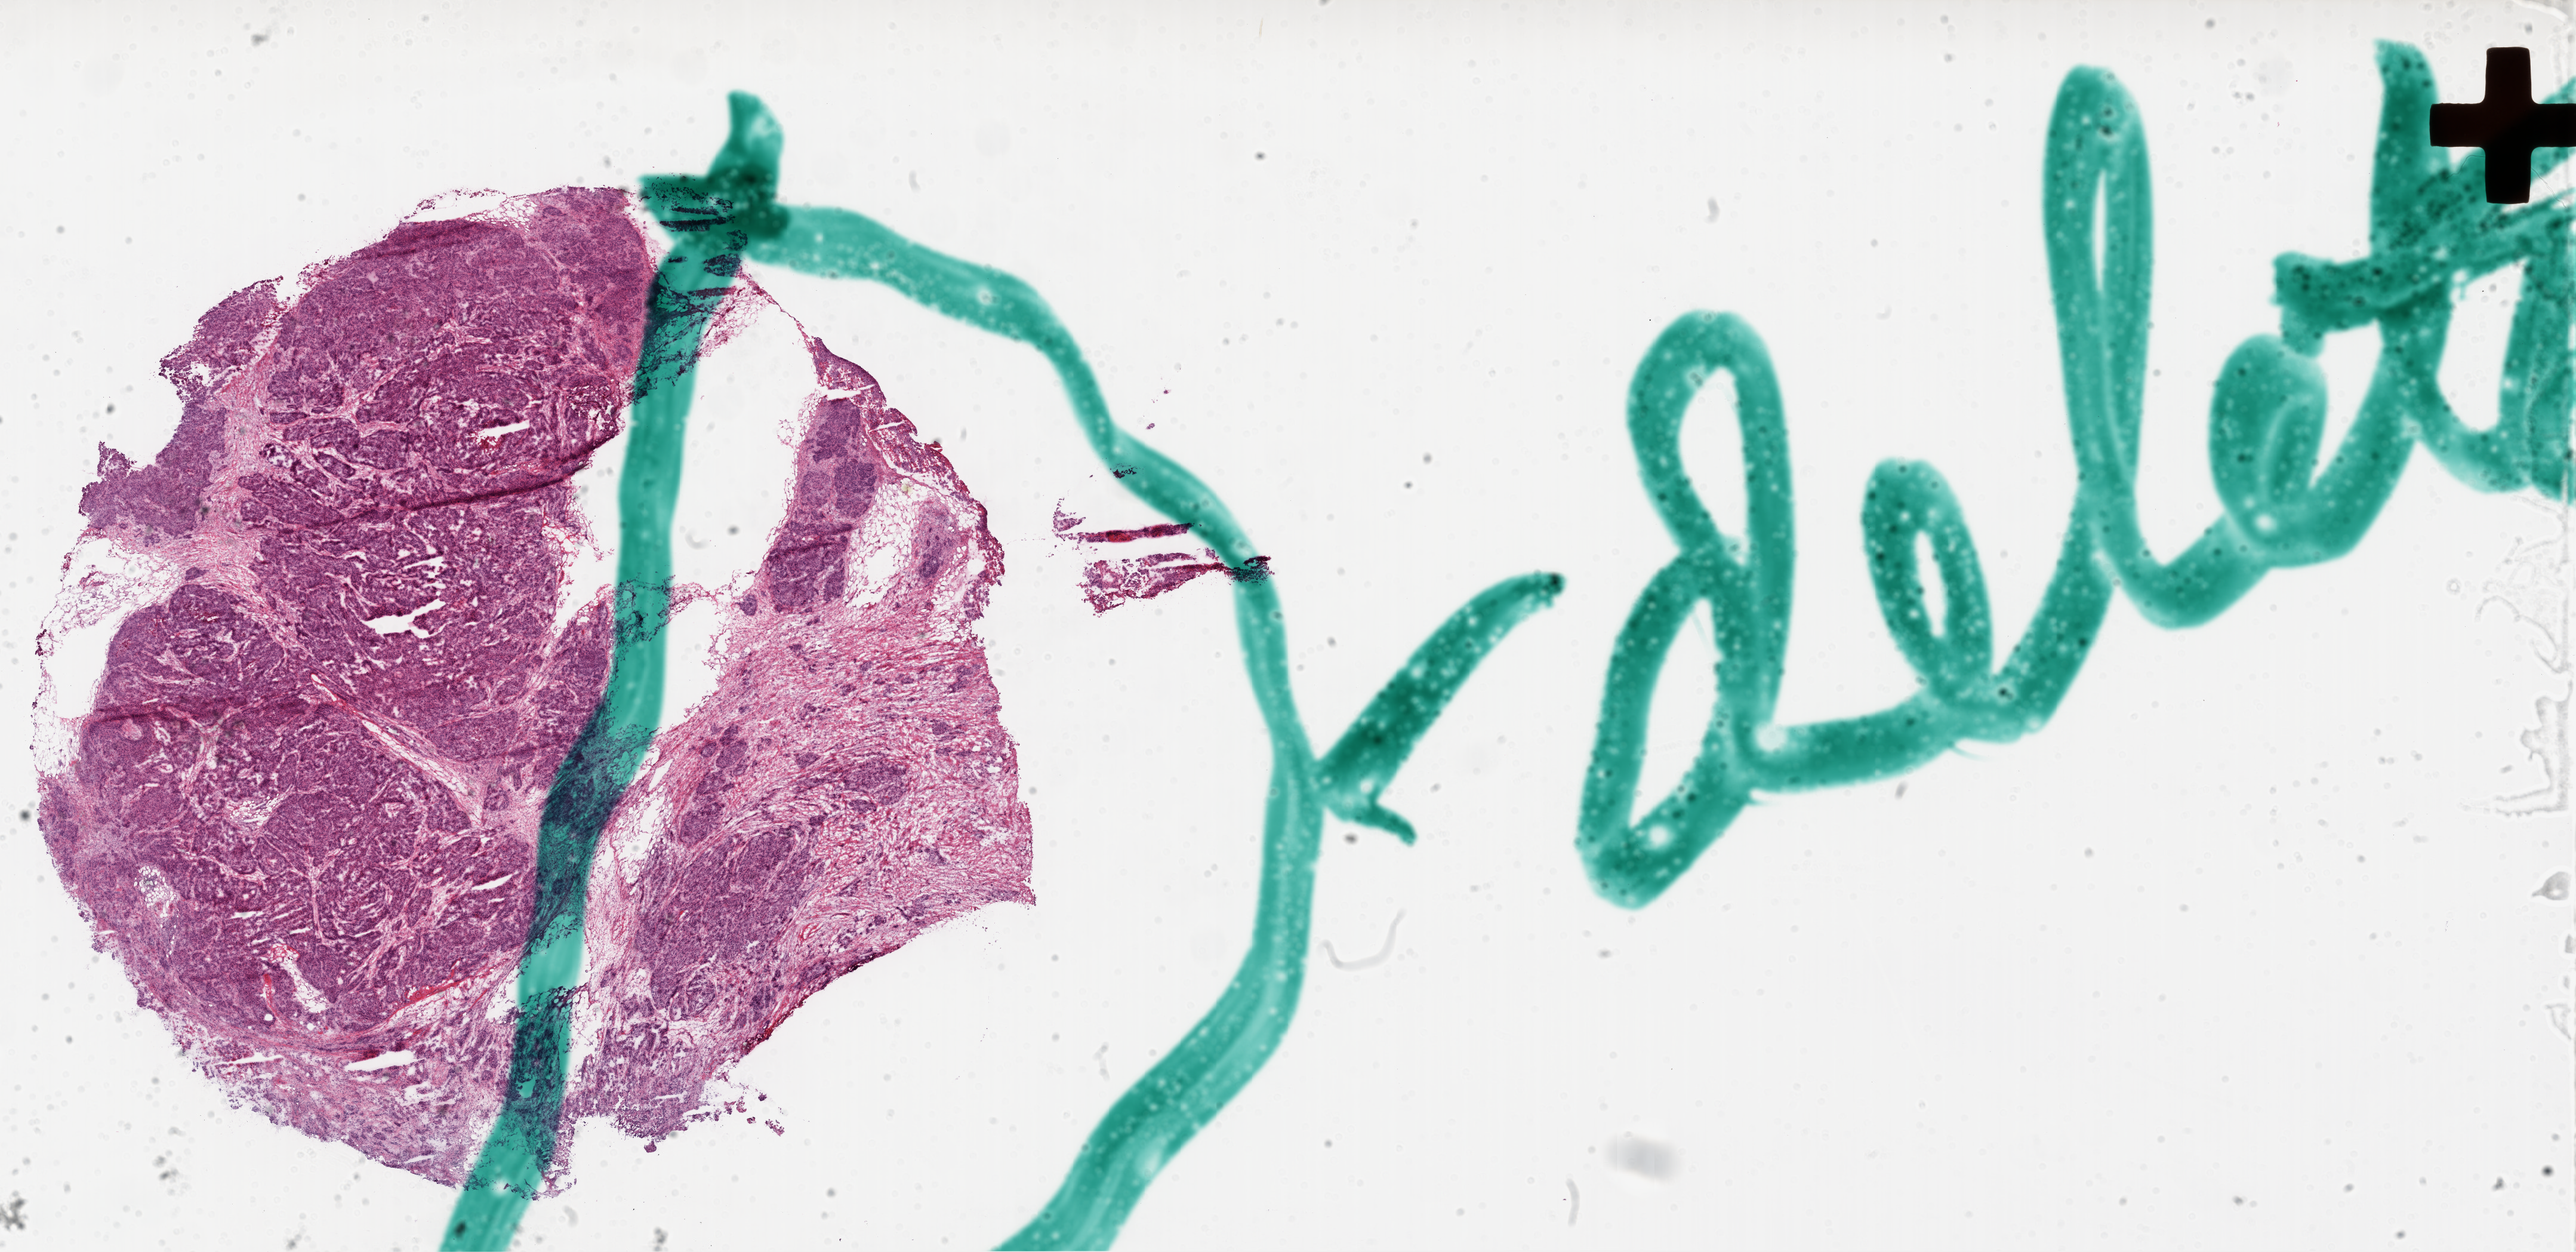
H&E-stained whole-slide image, low-resolution overview of the scanned area, about 34.8 x 16.9 mm (slide scanned at 20x), frozen section from the top of the tissue portion, sample: primary tumour, ovary. Female patient; age at initial diagnosis 60 years. Slide review estimates, as recorded: tumour cells 84%, tumour nuclei 89%.
Histologic diagnosis: Serous cystadenocarcinoma, NOS.